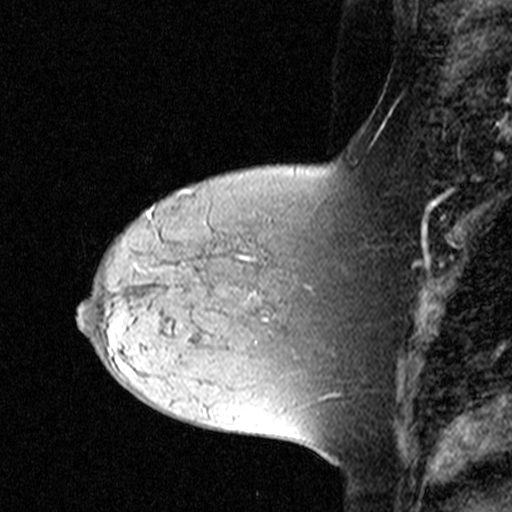
Breast MRI (dynamic contrast-enhanced), one sagittal slice. Slice 13 of 44 in the series (ordered by position). Dynamic contrast-enhanced study with each time point stored as its own series, time point 2 of 3 at this slice position (early post-contrast, ordered by acquisition time). 1.5 T. TE 4.5 ms, TR 11 ms. 3 mm slice thickness. 512 × 512 image matrix. Female patient, age 44 years. From the clinical record (not read from this slice): setting: breast cancer imaged before/during neoadjuvant chemotherapy; receptor status: triple-negative.
Structures marked on this image (semi-automatic segmentation, software-assisted and operator-edited):
- analysis volume of interest (the breast-tissue region the enhancement analysis was run in; not a lesion): bounding box [x1, y1, x2, y2] px = [132, 212, 309, 331]
- tumour enhancement mask (voxels above the 90 % enhancement threshold inside the analysis volume of interest): [146, 212, 150, 217]